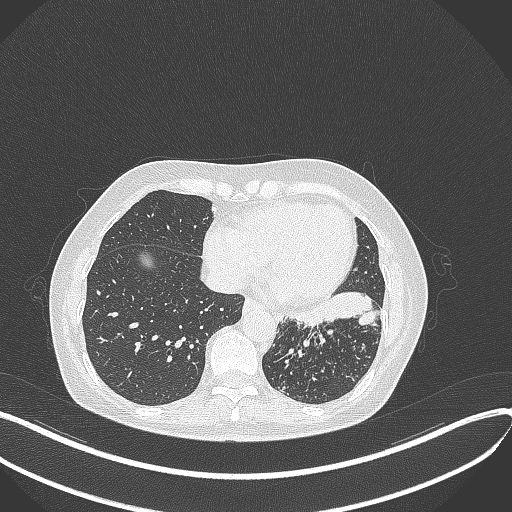
Chest CT, one axial slice. Slice 129 of 429 in the series (ordered by position). 100 kVp. Lung window (W 1500 / L -600 HU). 1 mm slice thickness. 512 × 512 image matrix. Female patient, age 63 years. From the clinical record (not read from this slice): clinical TNM (as recorded): T1b N0 M0; histopathological grade: G2-3.
Outlined on this slice (bounding box drawn by a radiologist):
- lung tumour (recorded histology: adenocarcinoma): bounding box <294,292,377,332> (left, top, right, bottom; pixels)